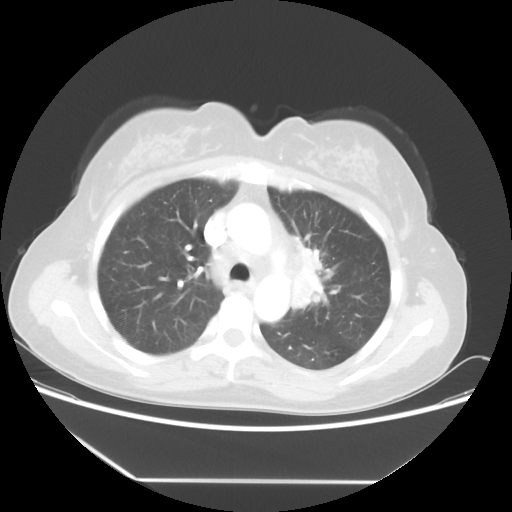
Chest CT, one axial slice. Slice 36 of 52 in the series (ordered by position). Reconstruction kernel STANDARD. 100 kVp. Lung window (W 1500 / L -600 HU). 5 mm slice thickness. 512 × 512 image matrix, field of view 390 × 390 mm. Patient: female, 50 years. Case-level facts recorded for this patient, not image findings: clinical TNM (as recorded): T2 N3 M0.
Outlined on this slice (rectangle marked by the reading radiologist):
- lung tumour (recorded histology: adenocarcinoma): bounding box (x1, y1, x2, y2) in pixels: (295, 239, 330, 320)